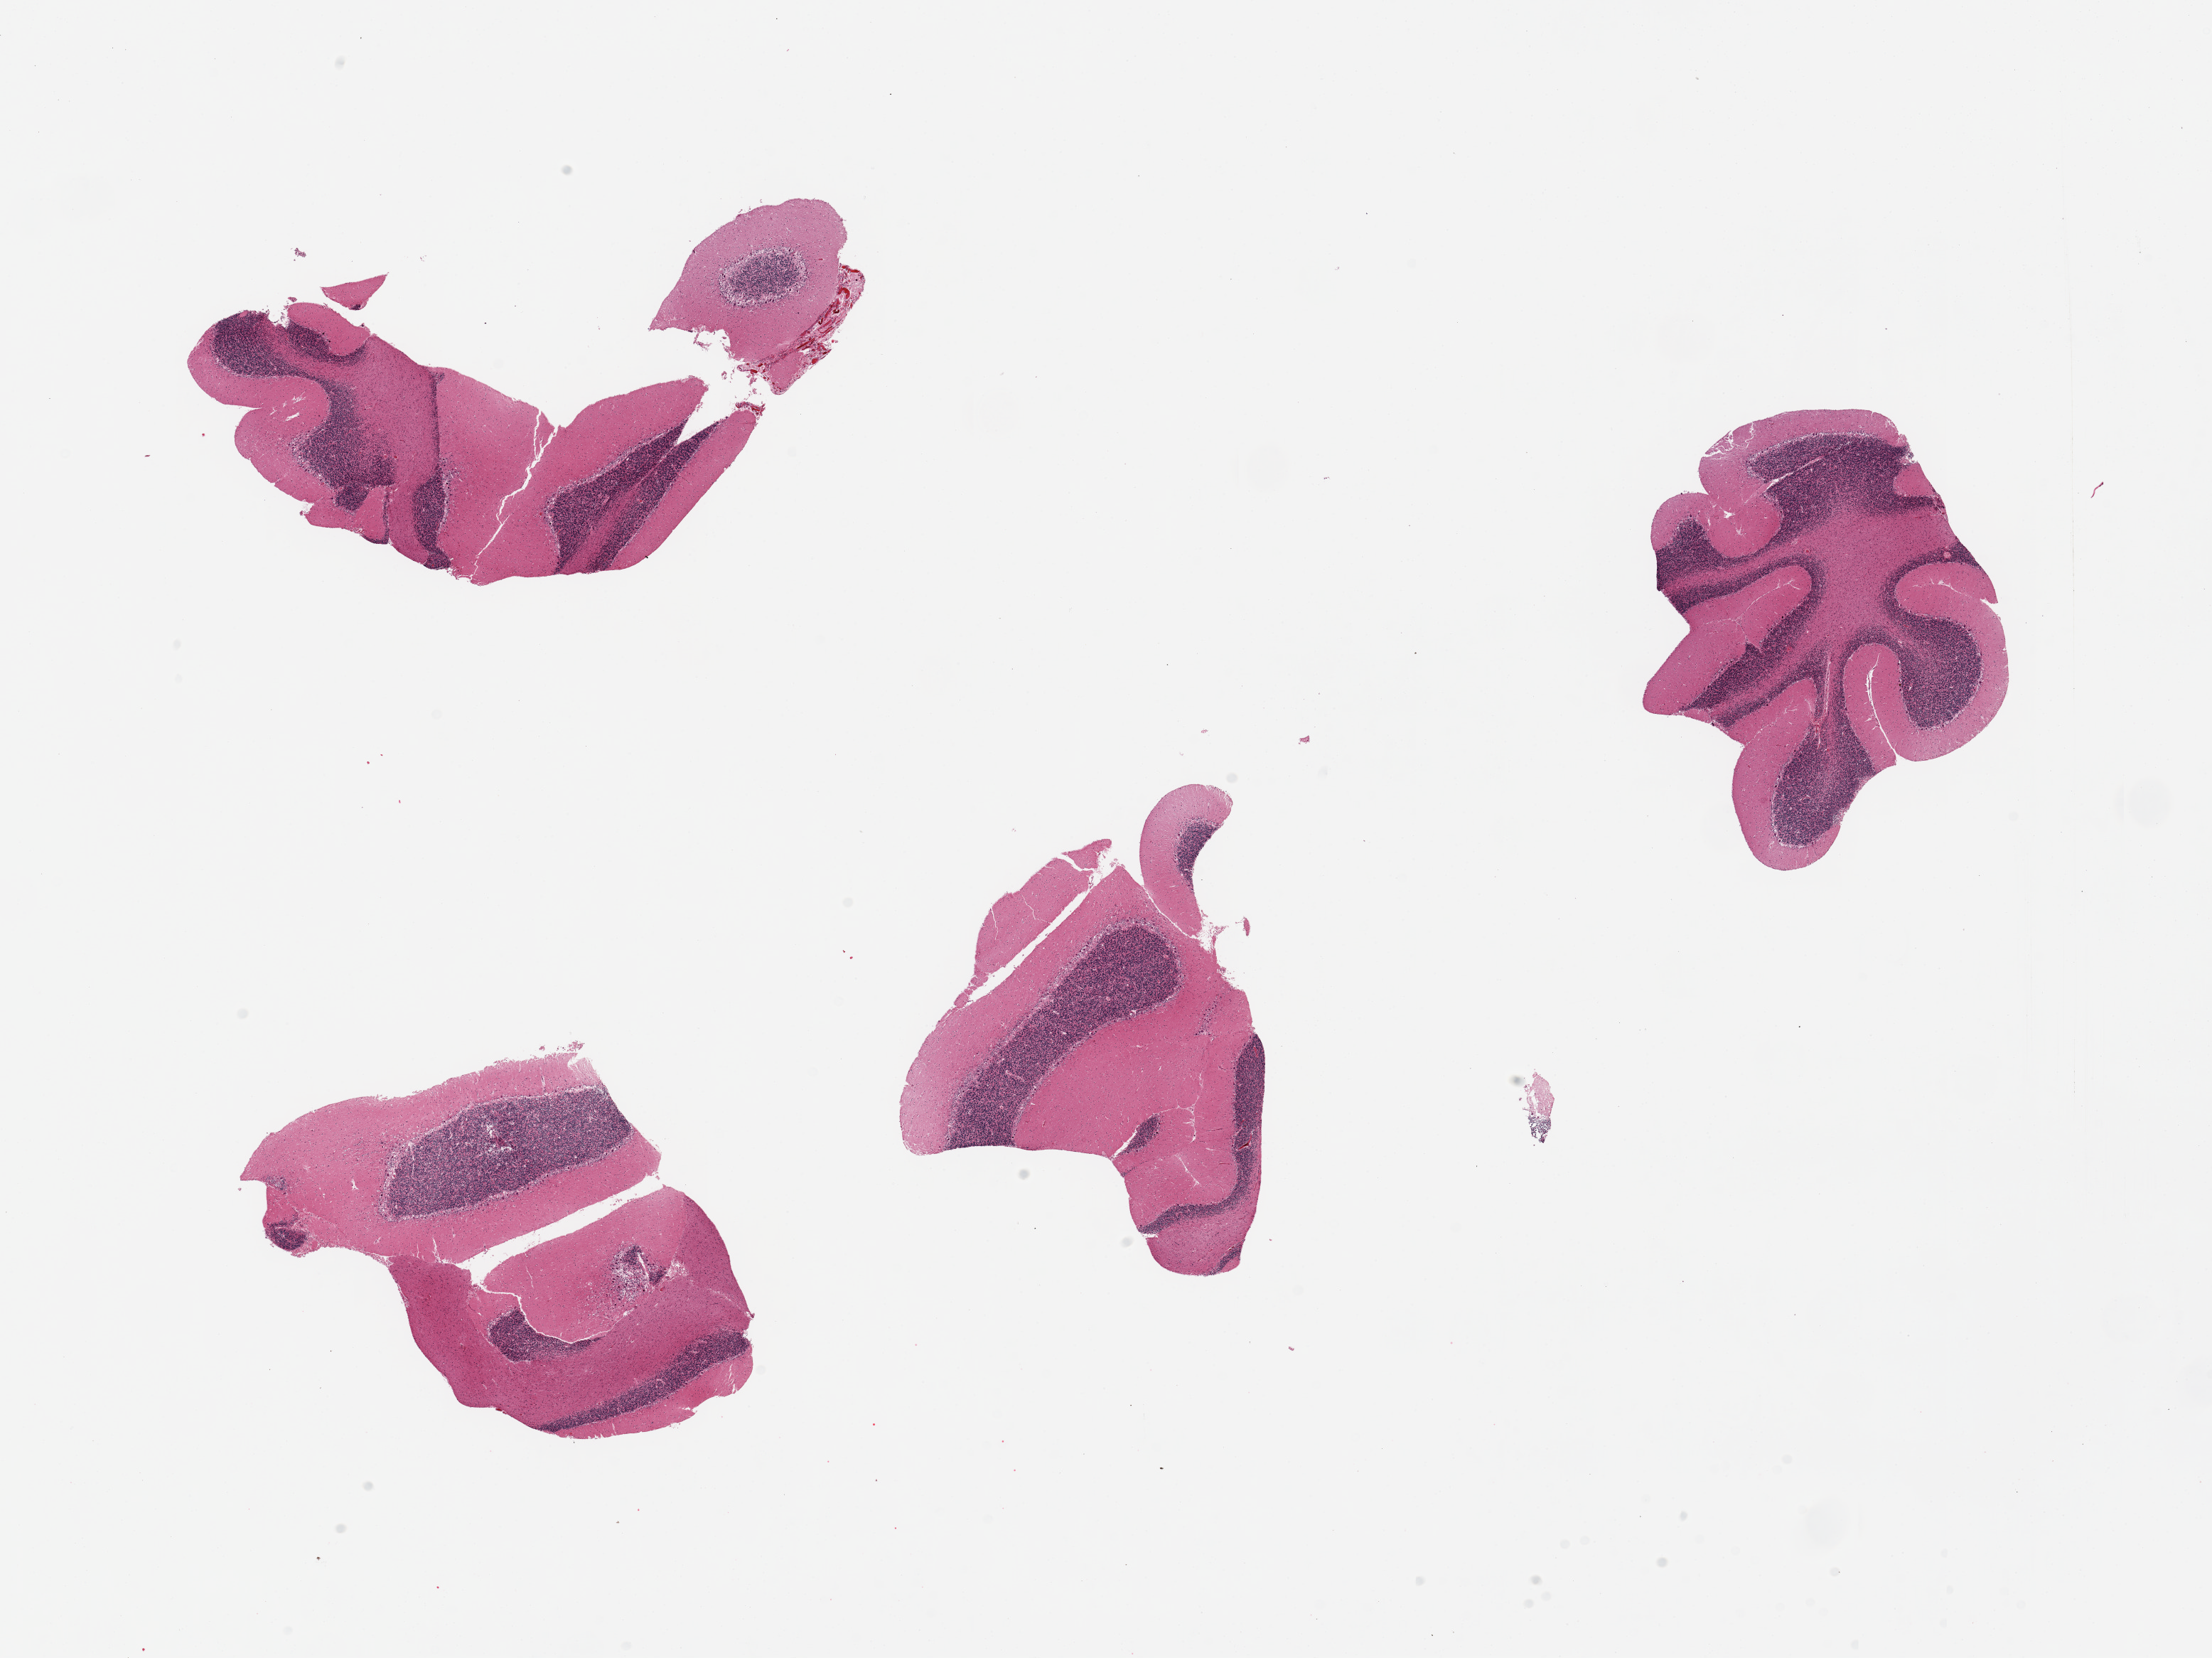
Digitized H&E-stained section, brightfield, whole scanned area (about 24.6 x 18.4 mm) shown as a low-resolution overview; PAXgene-fixed, paraffin-embedded tissue; section of cerebellum (target tissue); tissue donor sample. Donor: male.
* pathologist's review note for this sample: 4 pieces; Purkinje cells present, few with changes suggestive of hypoxic damage